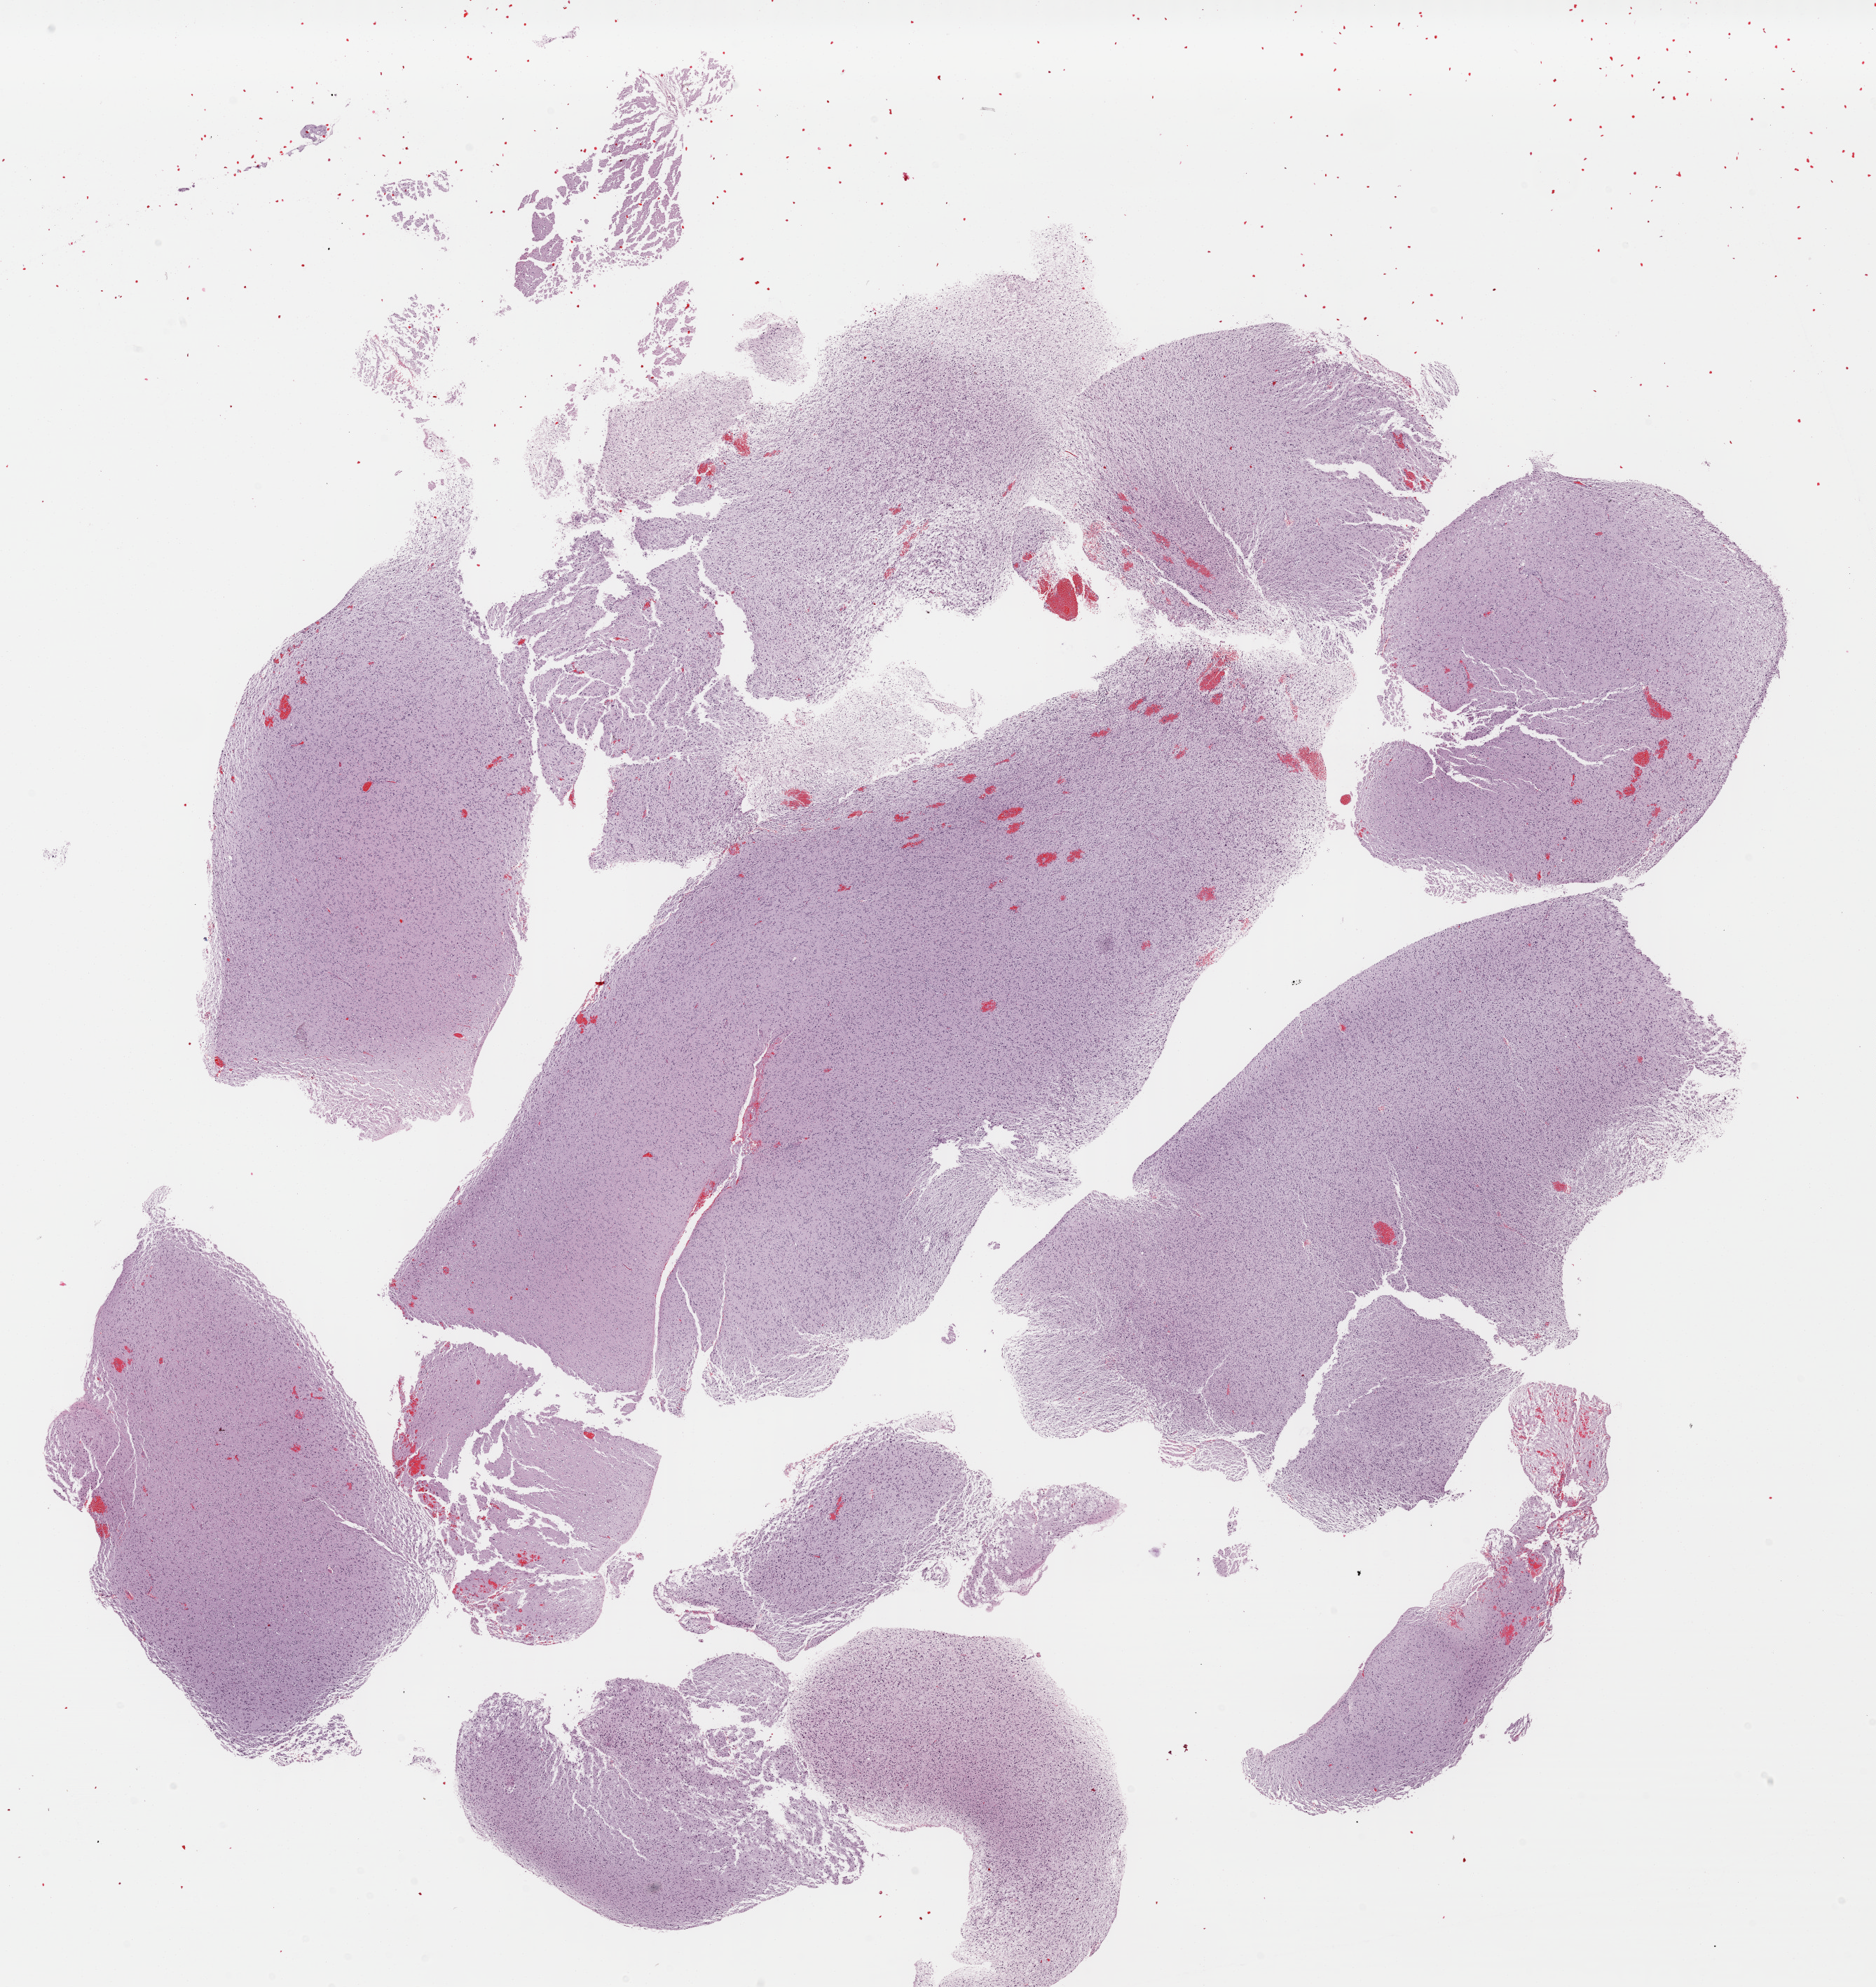
Digitized H&E-stained tissue section (whole slide) — whole scanned area (about 21.0 x 22.3 mm) shown as a low-resolution overview, FFPE section, primary tumour sample from the brain. Female patient; age at initial diagnosis 34 years. Histologic grade: G3 (poorly differentiated).
- laterality: left
- diagnosis: Astrocytoma, anaplastic